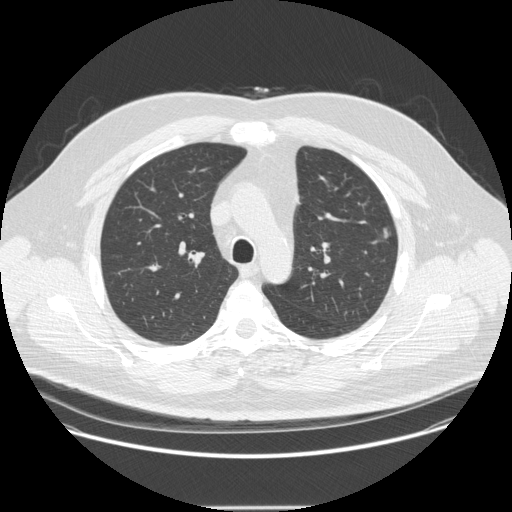
Chest CT (low-dose screening protocol), one axial image, second screening round (one year after baseline), lung window (W 1500 / L -600 HU), standard (soft-tissue) reconstruction kernel (STANDARD). Male participant, aged 55 years at enrolment. Former smoker at enrolment.
Lesion marked by an expert reader, bounding box [x1, y1, x2, y2] px = [373, 223, 407, 250]. The screening reader recorded 2 non-calcified nodules or masses ≥4 mm on this exam (left upper lobe, left upper lobe); which of them this box marks is not recorded. Official screen result: positive, other. Lung cancer was diagnosed 60 days after this screen: adenocarcinoma, NOS, left upper lobe, moderately differentiated (G2), stage IA (AJCC 6th edition), 9 mm at pathology.